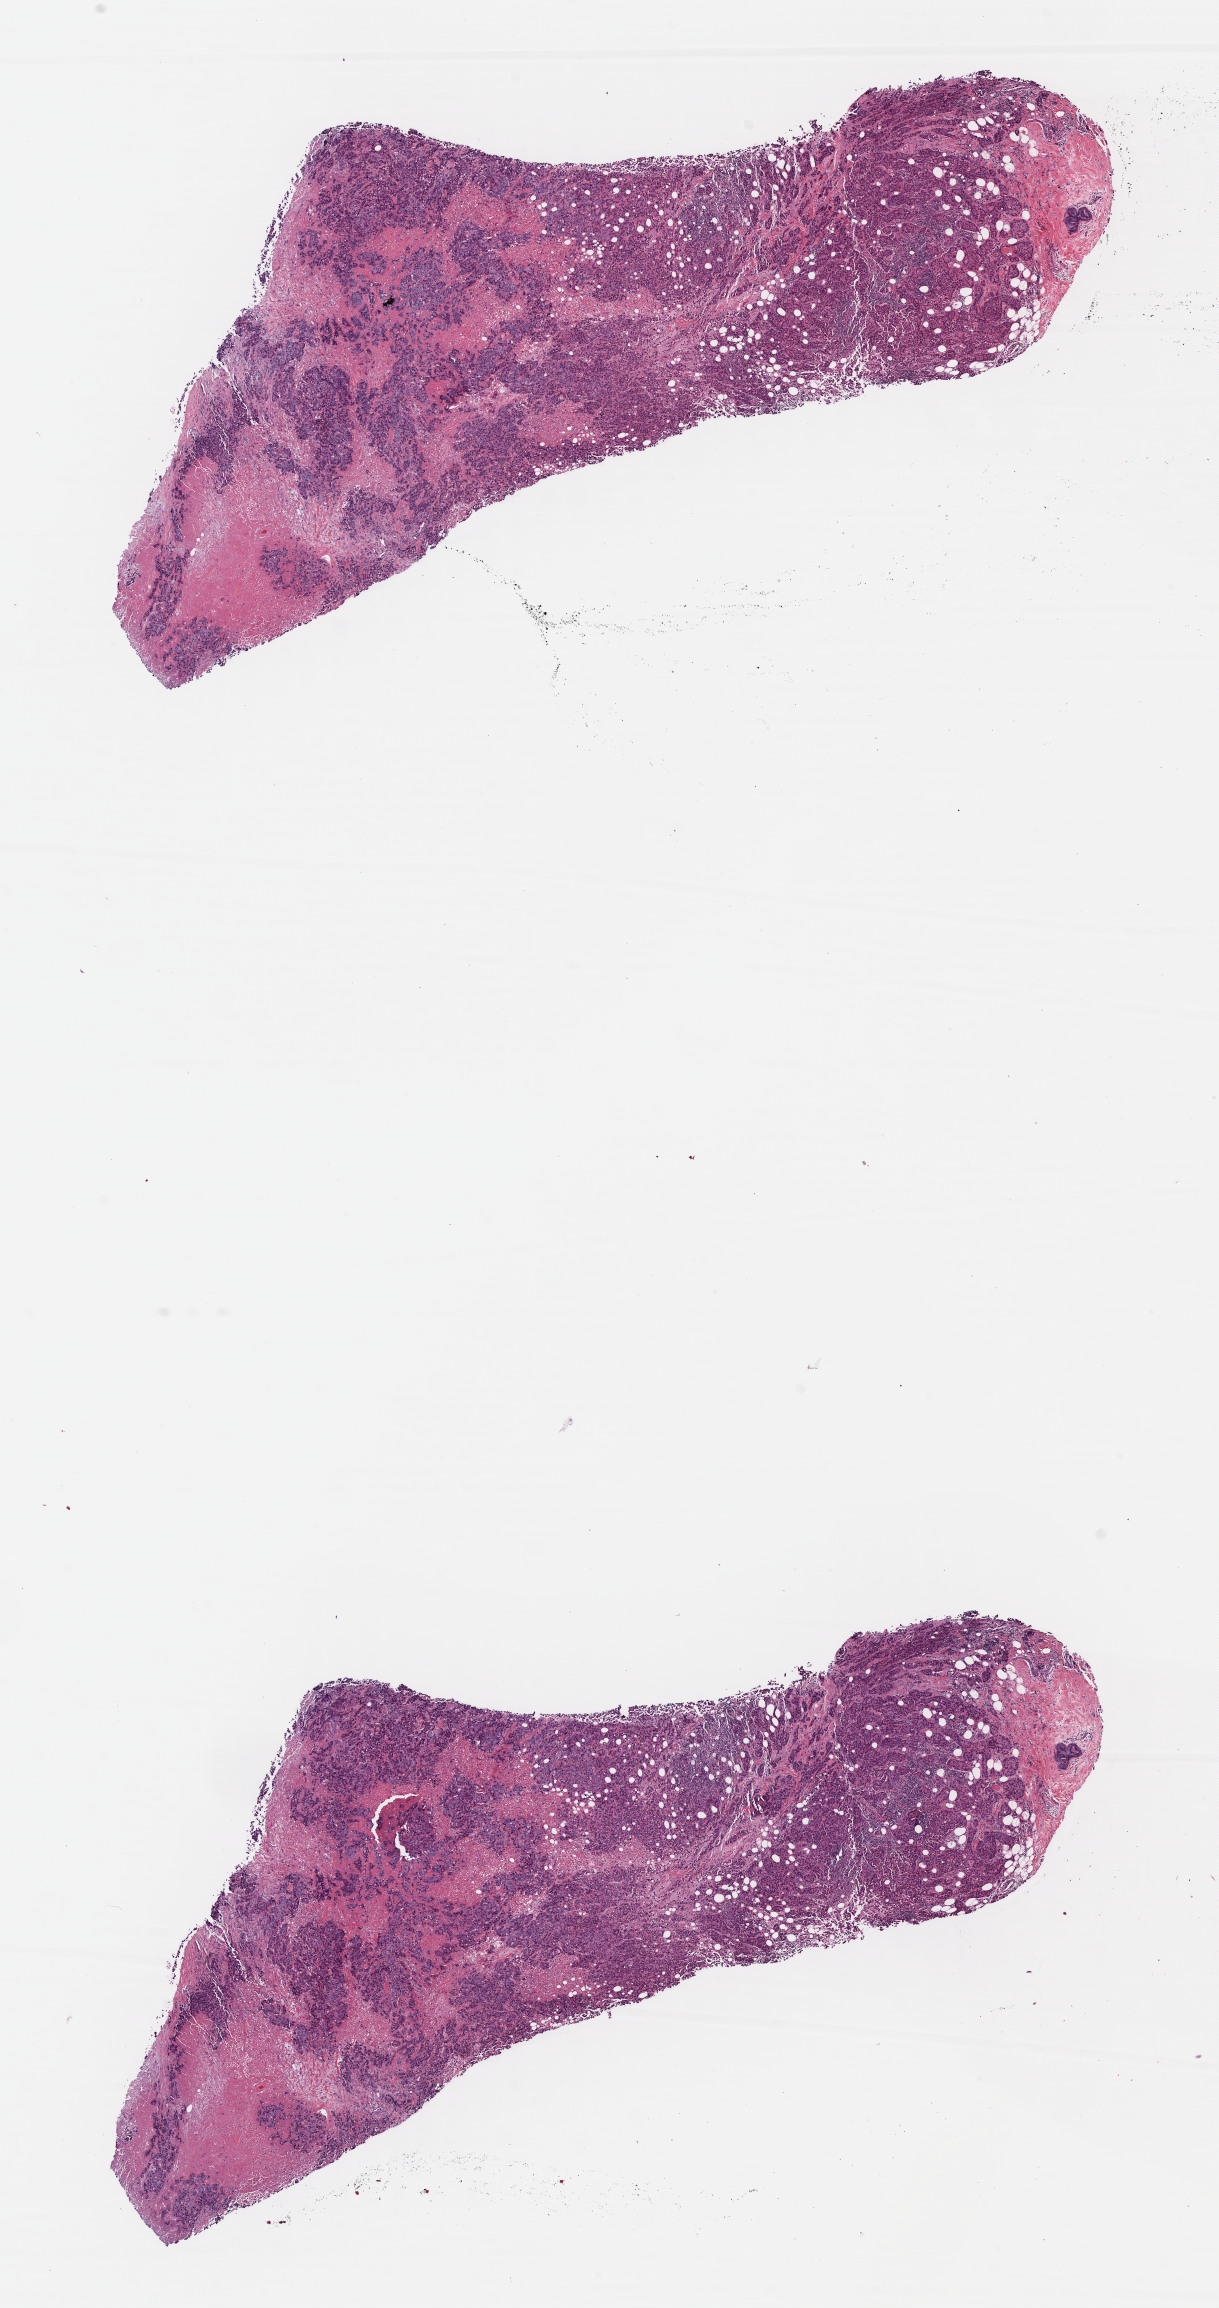
Whole-slide histology image, Hematoxylin and eosin (H&E) stained, low-resolution overview of the scanned area, about 9.6 x 18.2 mm, formalin-fixed paraffin-embedded (FFPE) diagnostic section, sample: primary tumour, breast. Female patient; age at initial diagnosis 57 years.
TNM: T2 N0 (i-) M0. Lymph nodes positive (case pathology): 0 of 1 examined. Diagnosis: Infiltrating duct carcinoma, NOS. AJCC pathologic stage: IIA. Laterality: left.